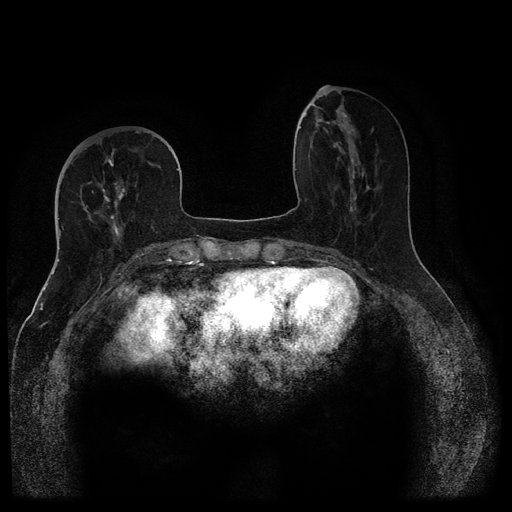
Breast MRI (dynamic contrast-enhanced, multi-phase), one axial slice. Slice 40 of 116 in the series (ordered by position). Dynamic contrast-enhanced series, time point 2 of 5 at this slice position (early post-contrast). 1.5 T. TE 2.6 ms, TR 5.4 ms. 2 mm slice thickness. 512 × 512 image matrix, field of view 340 × 340 mm. Patient: female, 68 years.
Annotated regions visible in this slice (semi-automatically segmented with operator editing):
- breast lesion (labelled benign in the annotation): bounding box [x1, y1, x2, y2] px = [335, 106, 351, 129]